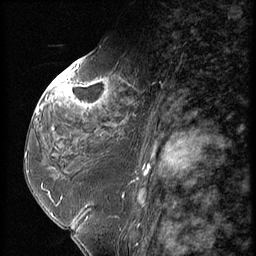
Breast MRI (dynamic contrast-enhanced), one sagittal slice. Position 30 of 56 along the scan axis. Dynamic contrast-enhanced series, image 2 of 3 at this slice position (ordered by acquisition). 1.5 T. TE 4.2 ms, TR 9 ms. 2.5 mm slice thickness. 256 × 256 image matrix, field of view 180 × 180 mm. Patient: female, 59 years. Case-level facts recorded for this patient, not image findings: setting: breast cancer imaged before/during neoadjuvant chemotherapy; receptor status: HER2-positive.
Outlined on this slice (semi-automatically segmented with operator editing):
- analysis volume of interest (the breast-tissue region the enhancement analysis was run in; not a lesion): bounding box [x1, y1, x2, y2] px = [44, 66, 151, 135]
- tumour enhancement mask (voxels above the 140 % enhancement threshold inside the analysis volume of interest): [52, 73, 105, 96]